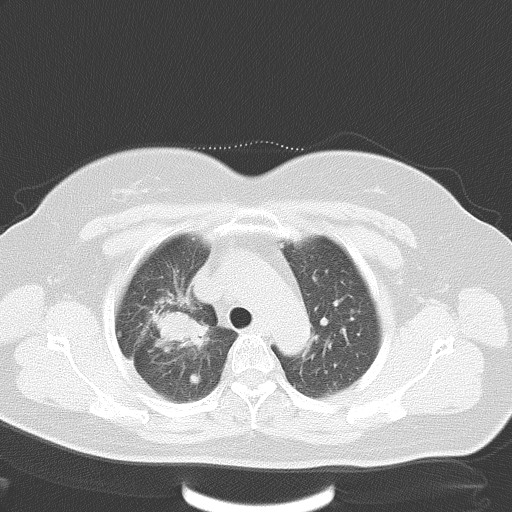
Chest CT, one axial slice. Position 38 of 48 along the scan axis. Reconstruction kernel B70f. Lung window (W 1500 / L -600 HU). 5 mm slice thickness. 512 × 512 image matrix, field of view 353 × 353 mm. Patient: female, 50 years. From the clinical record (not read from this slice): clinical TNM (as recorded): T2a N0 M1a.
Outlined on this slice (bounding box drawn by a radiologist):
- lung tumour (recorded histology: adenocarcinoma): bounding box [x1, y1, x2, y2] px = [151, 310, 215, 352]